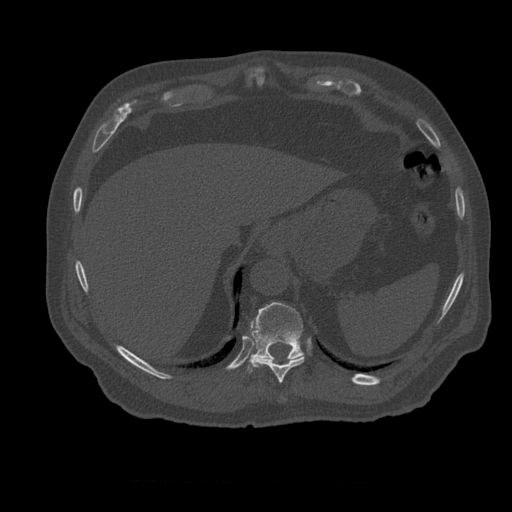
CT including the spine, one axial slice; position 292 of 399 along the scan axis; reconstruction kernel STANDARD; 120 kVp; bone window (W 1800 / L 400 HU); 1.25 mm slice thickness; 512 × 512 image matrix. Patient age 73 years. From the clinical record (not read from this slice): primary cancer: prostate; vertebrae with lytic lesions (as recorded): L2.
Annotated regions visible in this slice (semi-automatically segmented with operator editing):
- T10 vertebra: bounding box (x1, y1, x2, y2) in pixels: (254, 356, 305, 383)
- T11 vertebra: (248, 302, 304, 373)